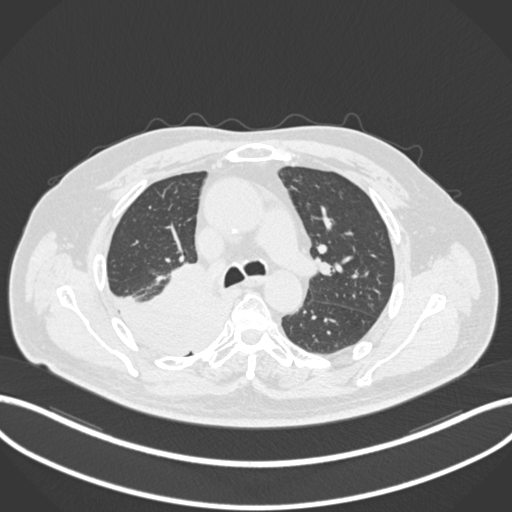
Chest CT, one axial slice; slice 132 of 218 in the series (ordered by position); 120 kVp; lung window (W 1500 / L -600 HU); 1 mm slice thickness; 512 × 512 image matrix, field of view 400 × 400 mm. Male patient, age 68 years. Case-level facts recorded for this patient, not image findings: clinical TNM (as recorded): T2a N0 M0.
Outlined on this slice (rectangle marked by the reading radiologist):
- lung tumour (recorded histology: adenocarcinoma): bounding box <110,264,226,355> (left, top, right, bottom; pixels)